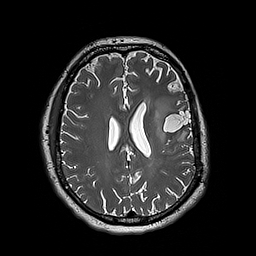
Brain MRI from a brain-tumour surgery series, one axial slice; position 82 of 192 along the scan axis; 1 mm slice thickness; 256 × 256 image matrix, field of view 250 × 250 mm. Case-level facts recorded for this patient, not image findings: histopathology: Astrocytoma; WHO grade: 3; IDH mutation: yes; tumour location: Left Insular.
Annotated regions visible in this slice (outlined manually by an expert reader):
- tumour: bounding box [x1, y1, x2, y2] px = [153, 96, 178, 144]